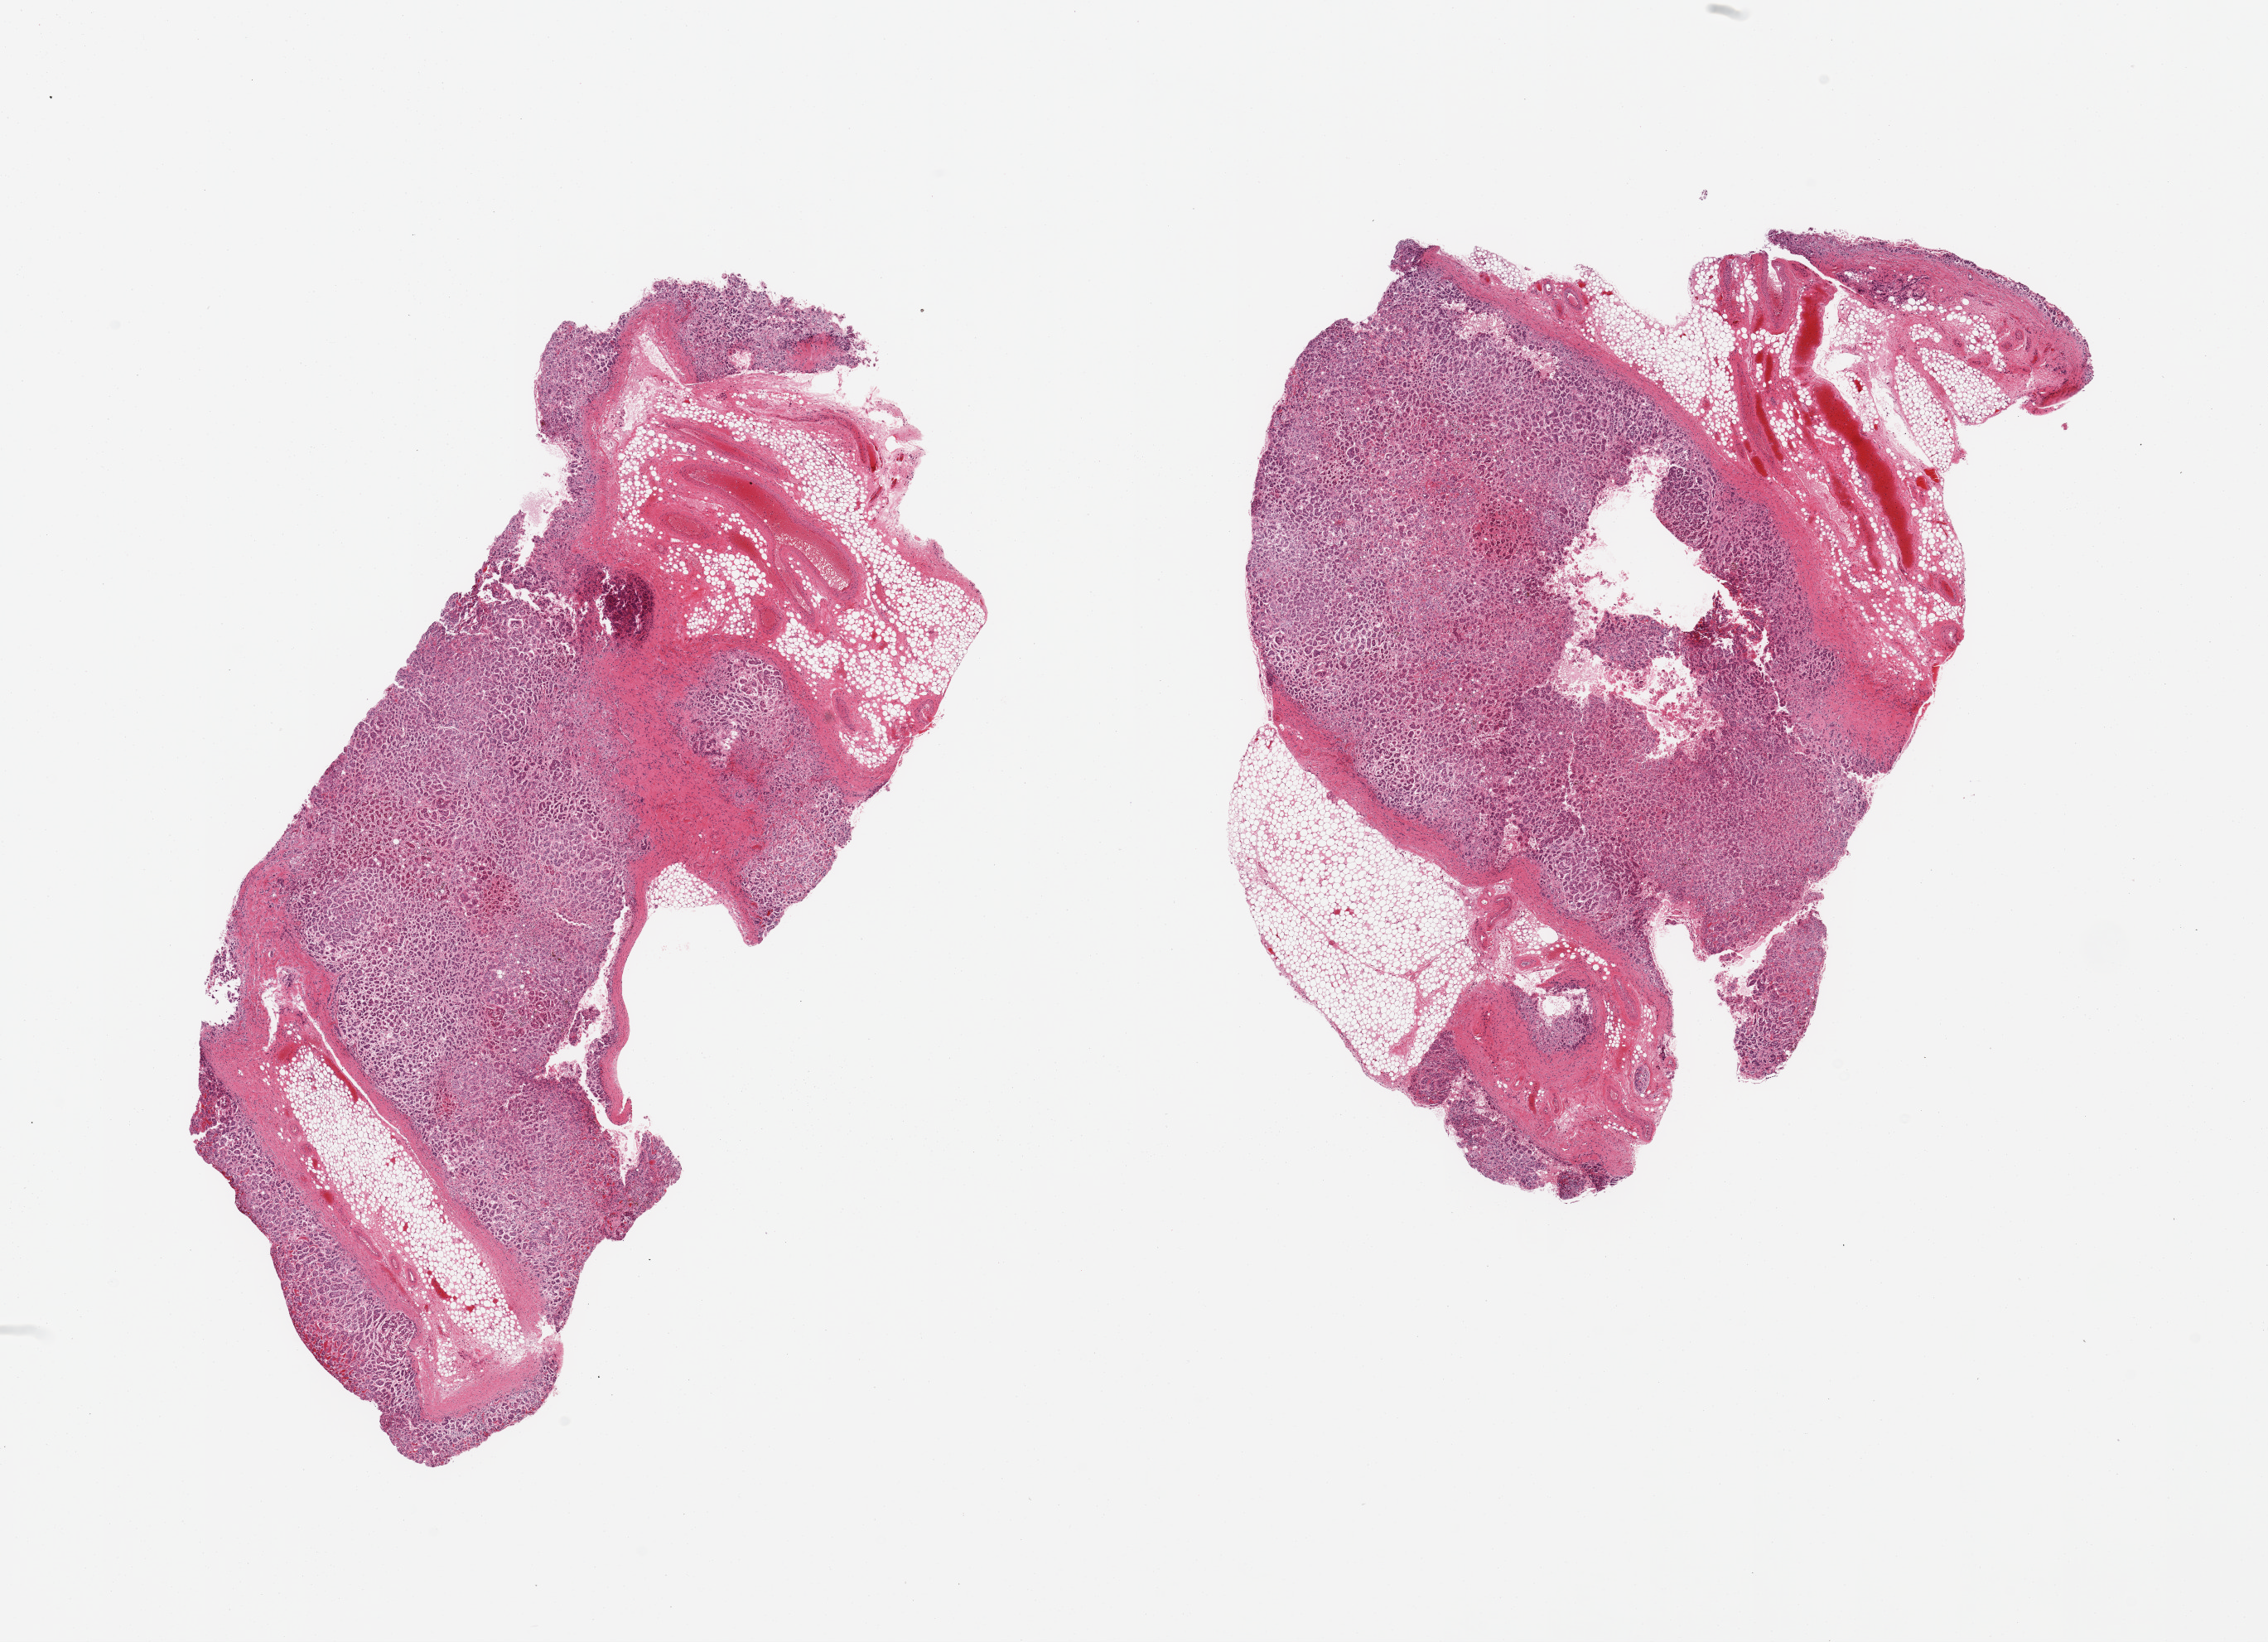
Whole-slide image, haematoxylin and eosin stain, a low-resolution overview of the entire scanned area, about 21.7 x 15.7 mm (slide scanned at 20x), PAXgene-fixed, paraffin-embedded tissue, section of adrenal gland (target tissue), tissue donor sample. Female donor.
Review note (as recorded): 2 pieces, ~60-70% cortex; rest is fat.